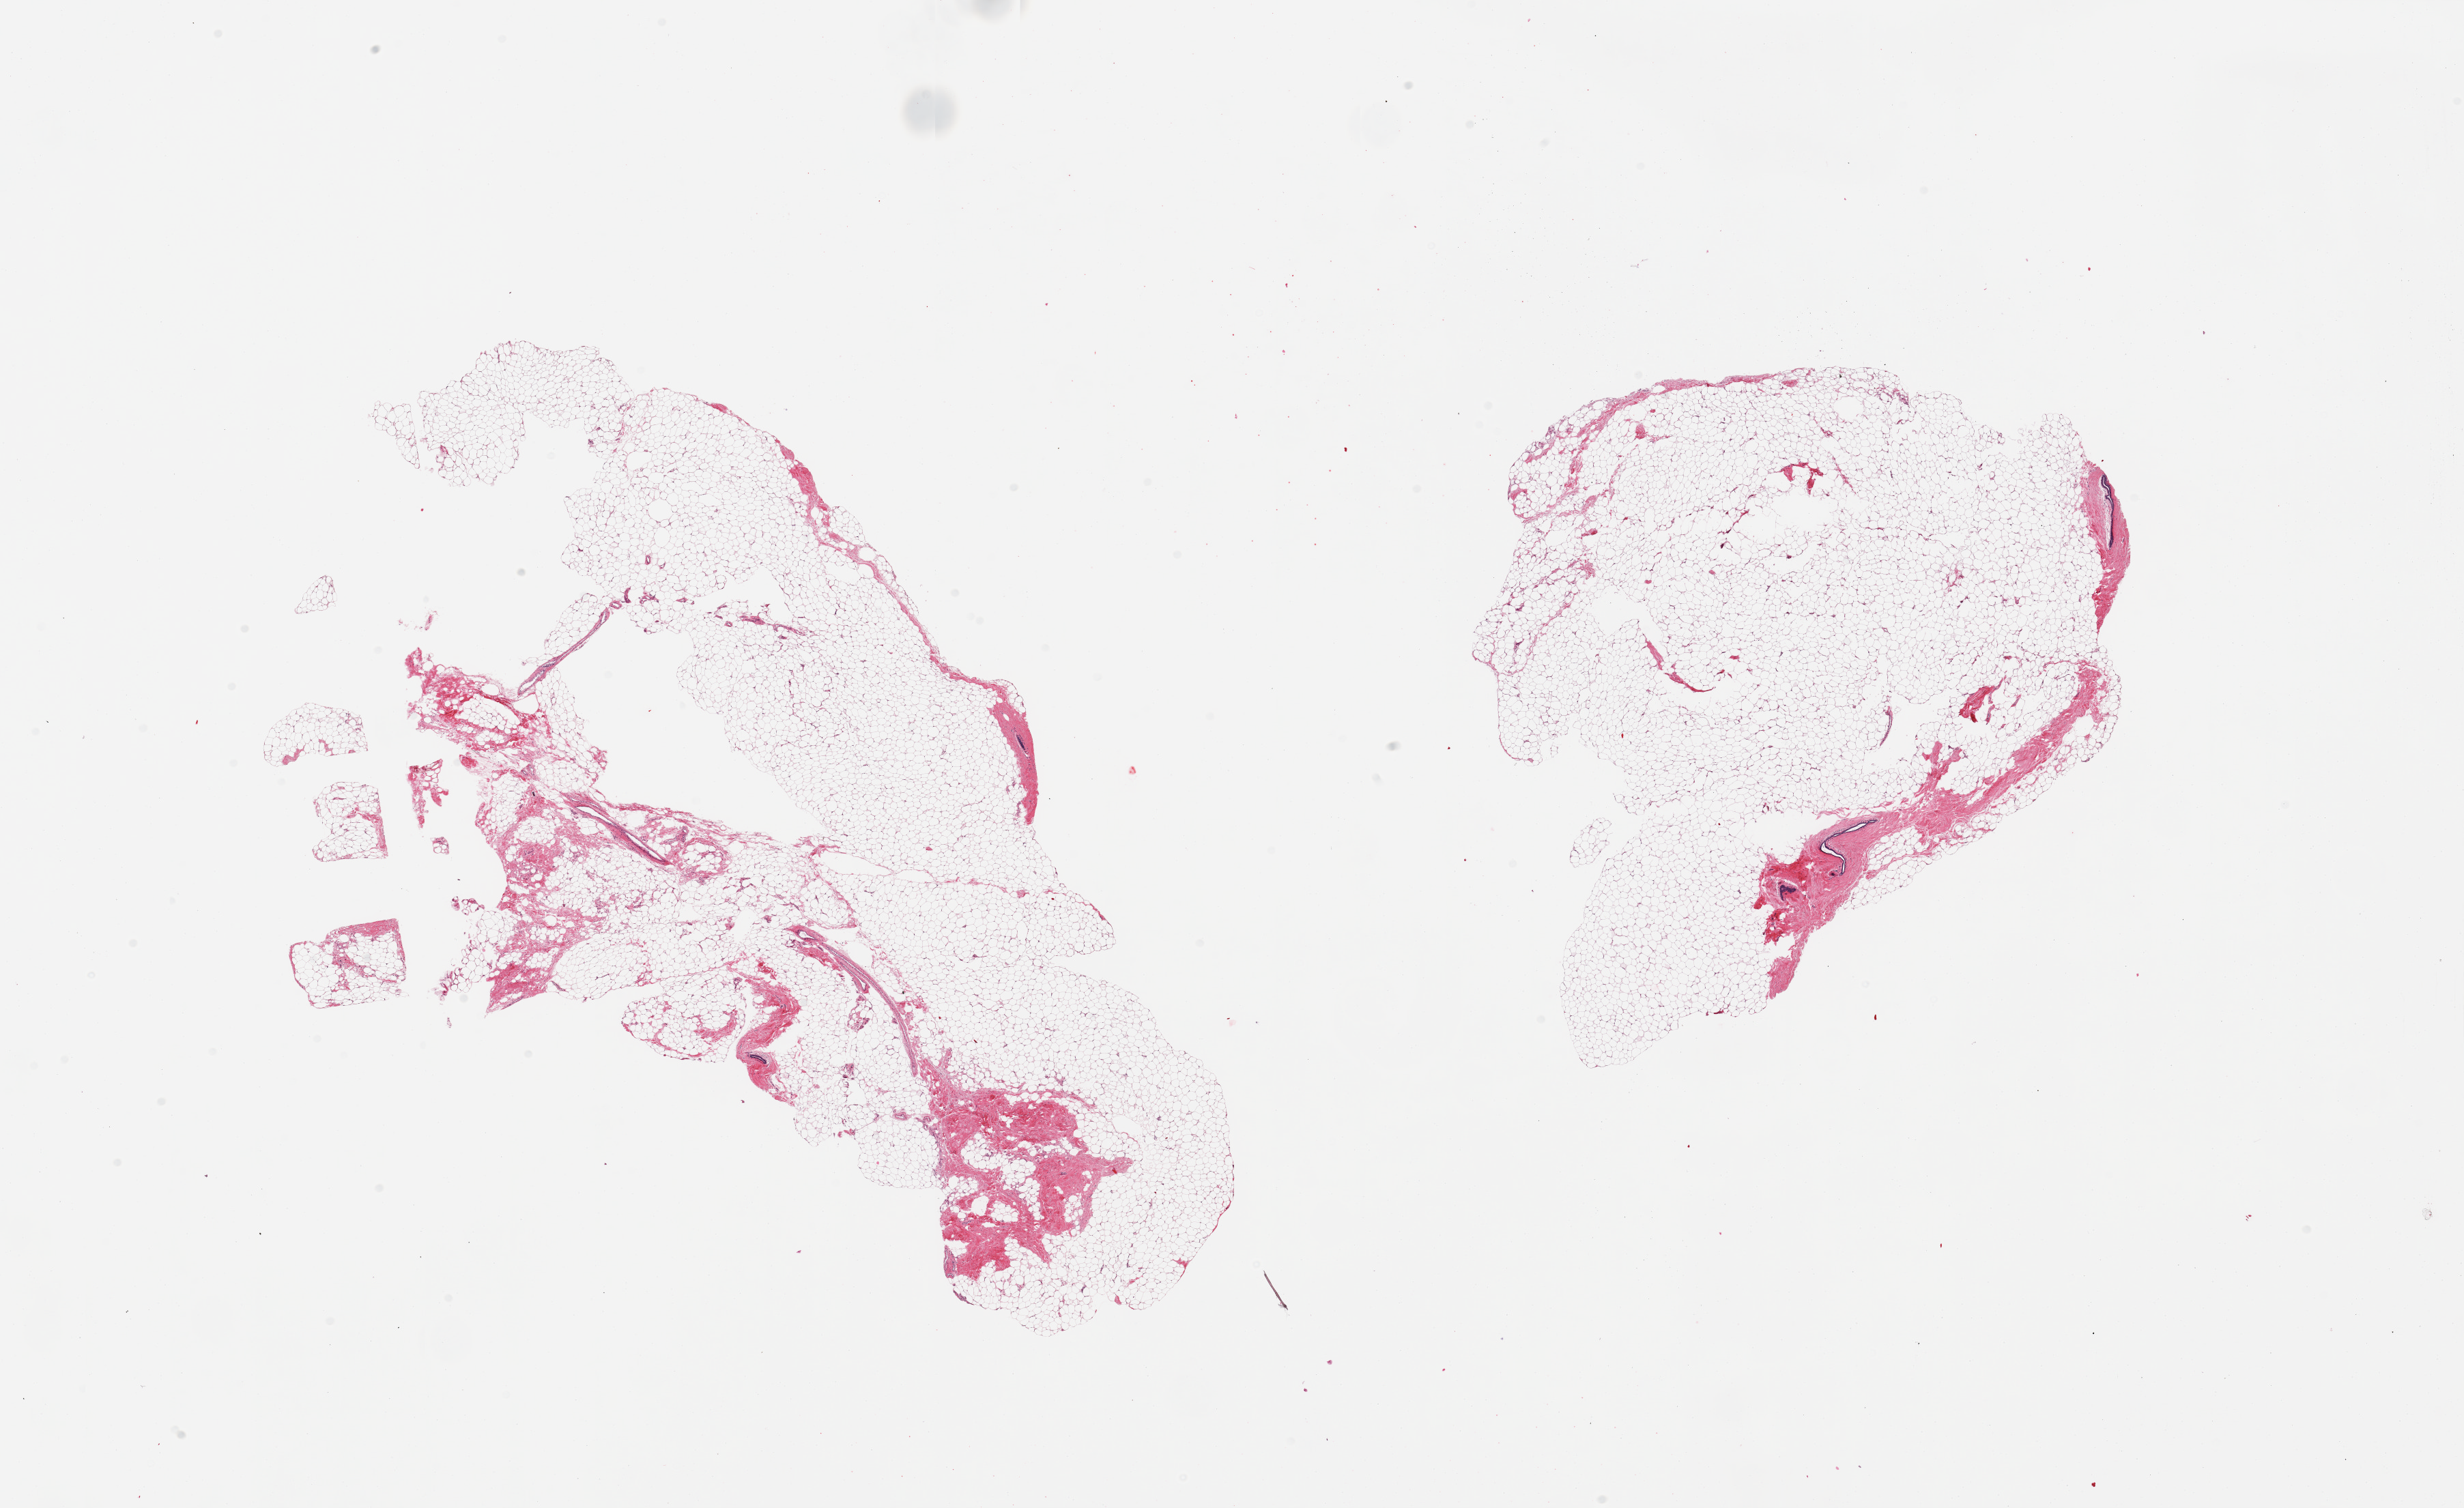
Whole-slide image, hematoxylin and eosin (H&E) stain, brightfield — low-resolution overview of the scanned area, about 28.5 x 17.5 mm (slide scanned at 20x), PAXgene-fixed paraffin-embedded (PFPE) section, target tissue: breast, donor tissue sample. Female donor.
* review note (as recorded): 2 pieces; 90% fat with scattered atrophic ducts, no lobules